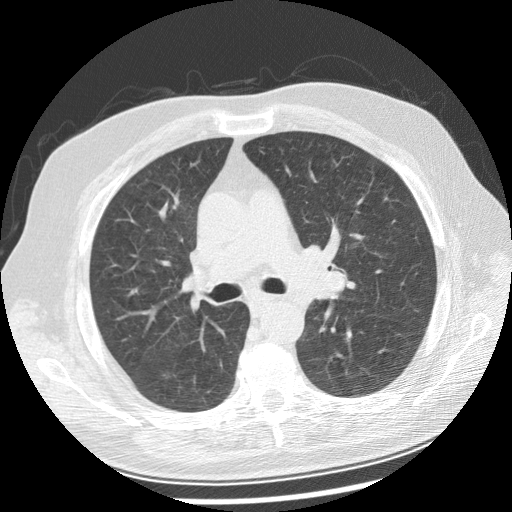
Low-dose screening chest CT, one axial slice; position 154 of 250 along the scan axis; reconstruction kernel STANDARD; 120 kVp; lung window (W 1500 / L -600 HU); 2.5 mm slice thickness; 512 × 512 image matrix.
Outlined on this slice (expert manual segmentation):
- lesion 1 (tumor, left main bronchus): bounding box <308,270,347,299> (left, top, right, bottom; pixels)